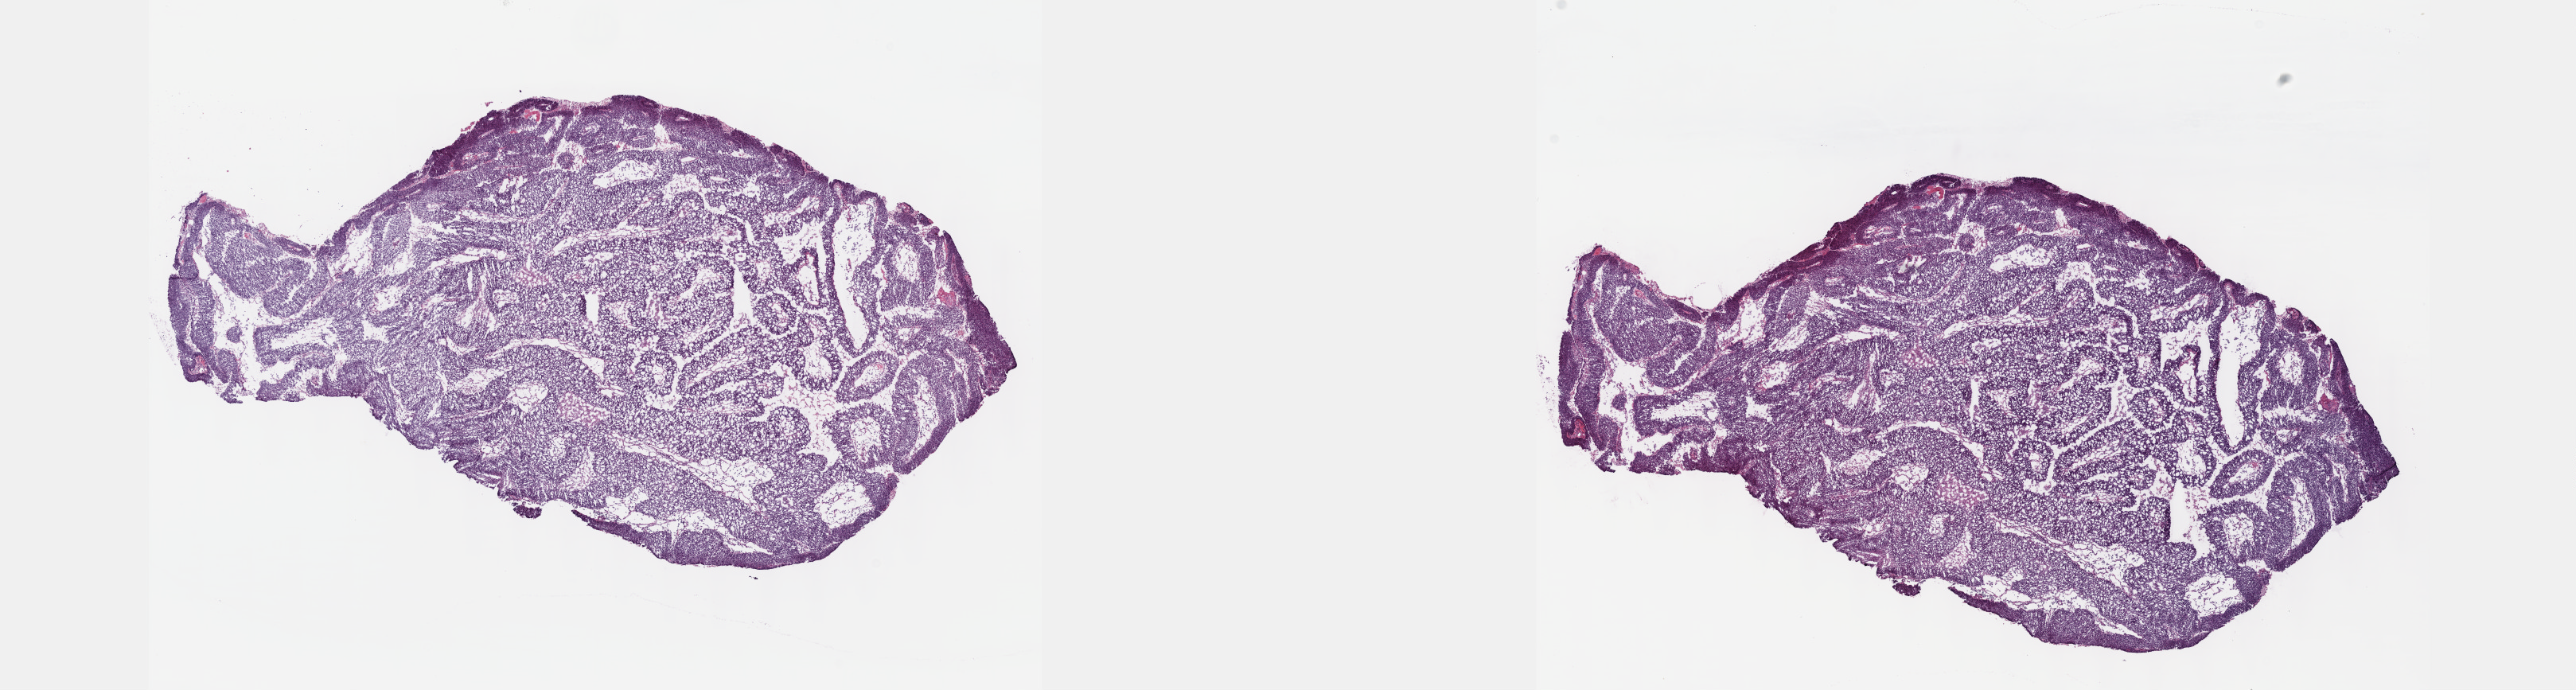
Whole-slide histology image, H&E, a low-resolution overview of the entire scanned area, about 26.2 x 7.0 mm (from a 40x scan); frozen section; cervix, primary tumour sample. Female, age 44 years at initial diagnosis. Slide review estimates, as recorded: tumour cells 70%, tumour nuclei 70%.
Pathologic diagnosis: Squamous cell carcinoma, NOS (cervix uteri).